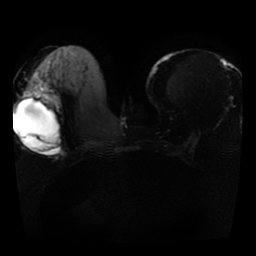
Breast MRI, one axial slice; slice 15 of 41 in the series (ordered by position); diffusion-weighted series; image 2 of 4 stored at this slice position (different b-values; order by instance number); 1.5 T; 5 mm slice thickness; 256 × 256 image matrix, field of view 330 × 330 mm. Female patient.
Structures marked on this image (outlined manually by an expert reader):
- tumour on diffusion-weighted imaging: box from (x=39, y=94) to (x=55, y=109) px